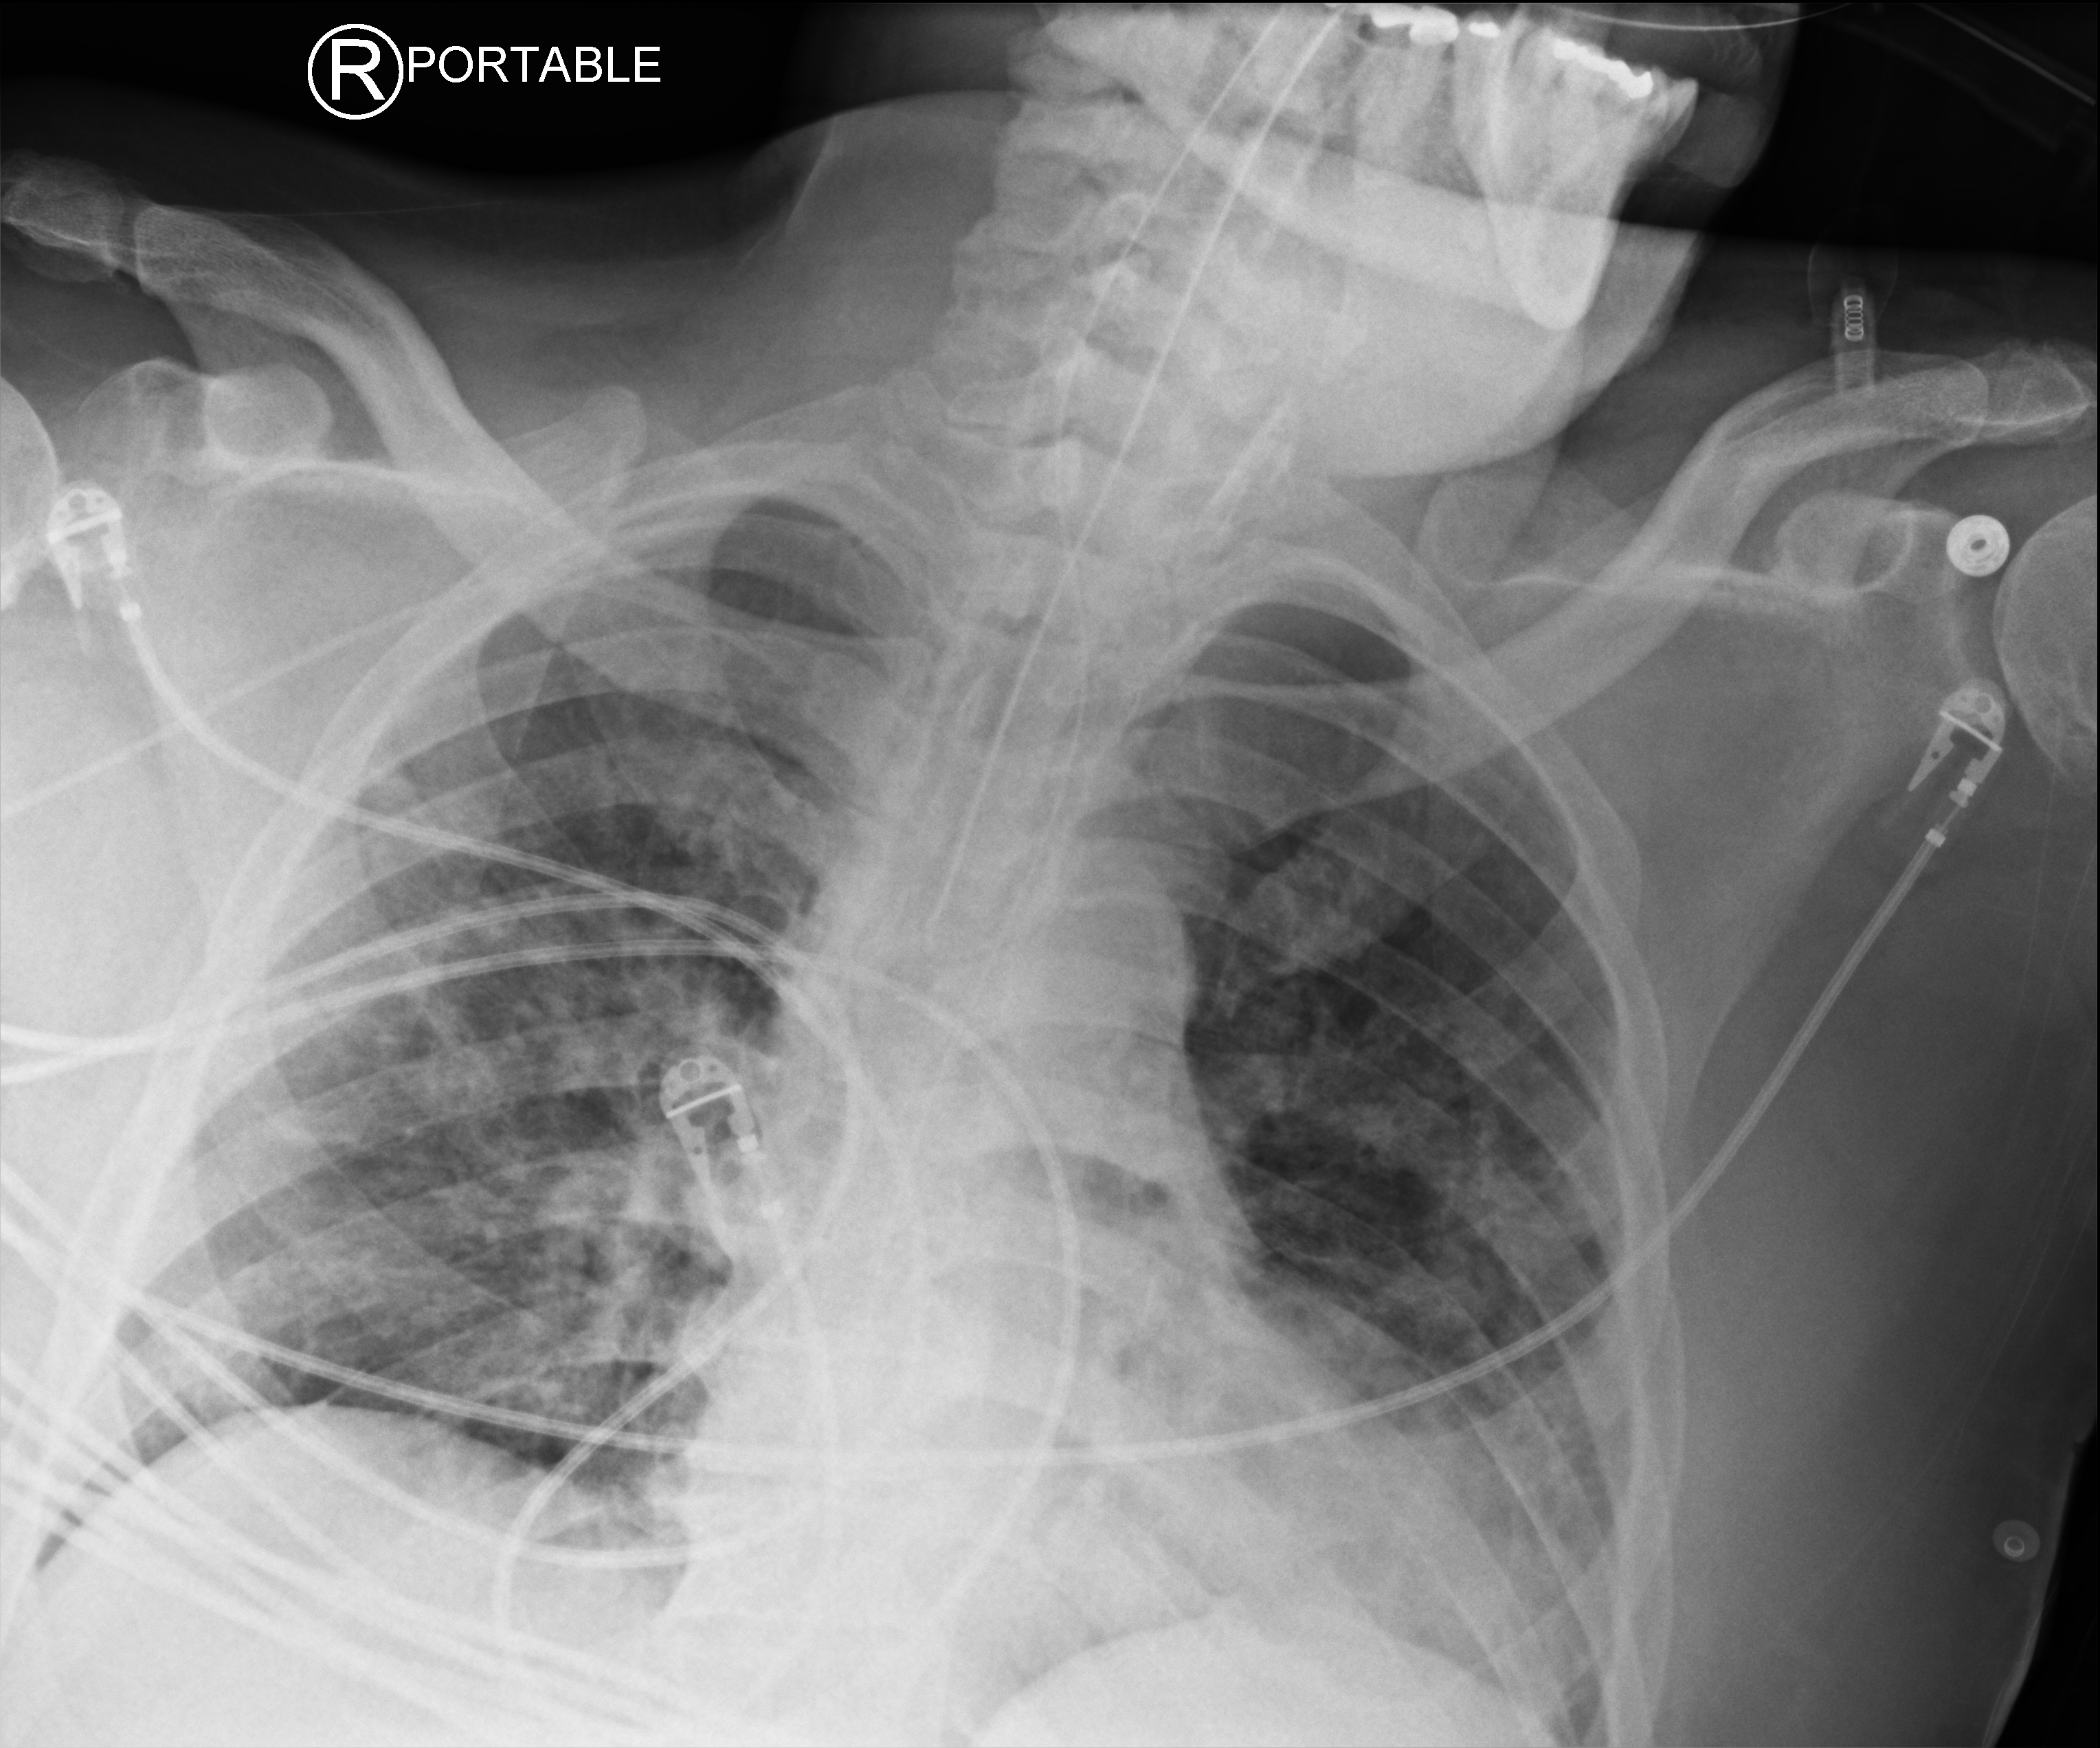
Chest X-ray (portable). Male patient hospitalised with COVID-19, age 18–59 years.
From the hospital-stay record, not from the radiograph (when in the stay this image was taken is not recorded):
- chronic kidney disease (admission record): no